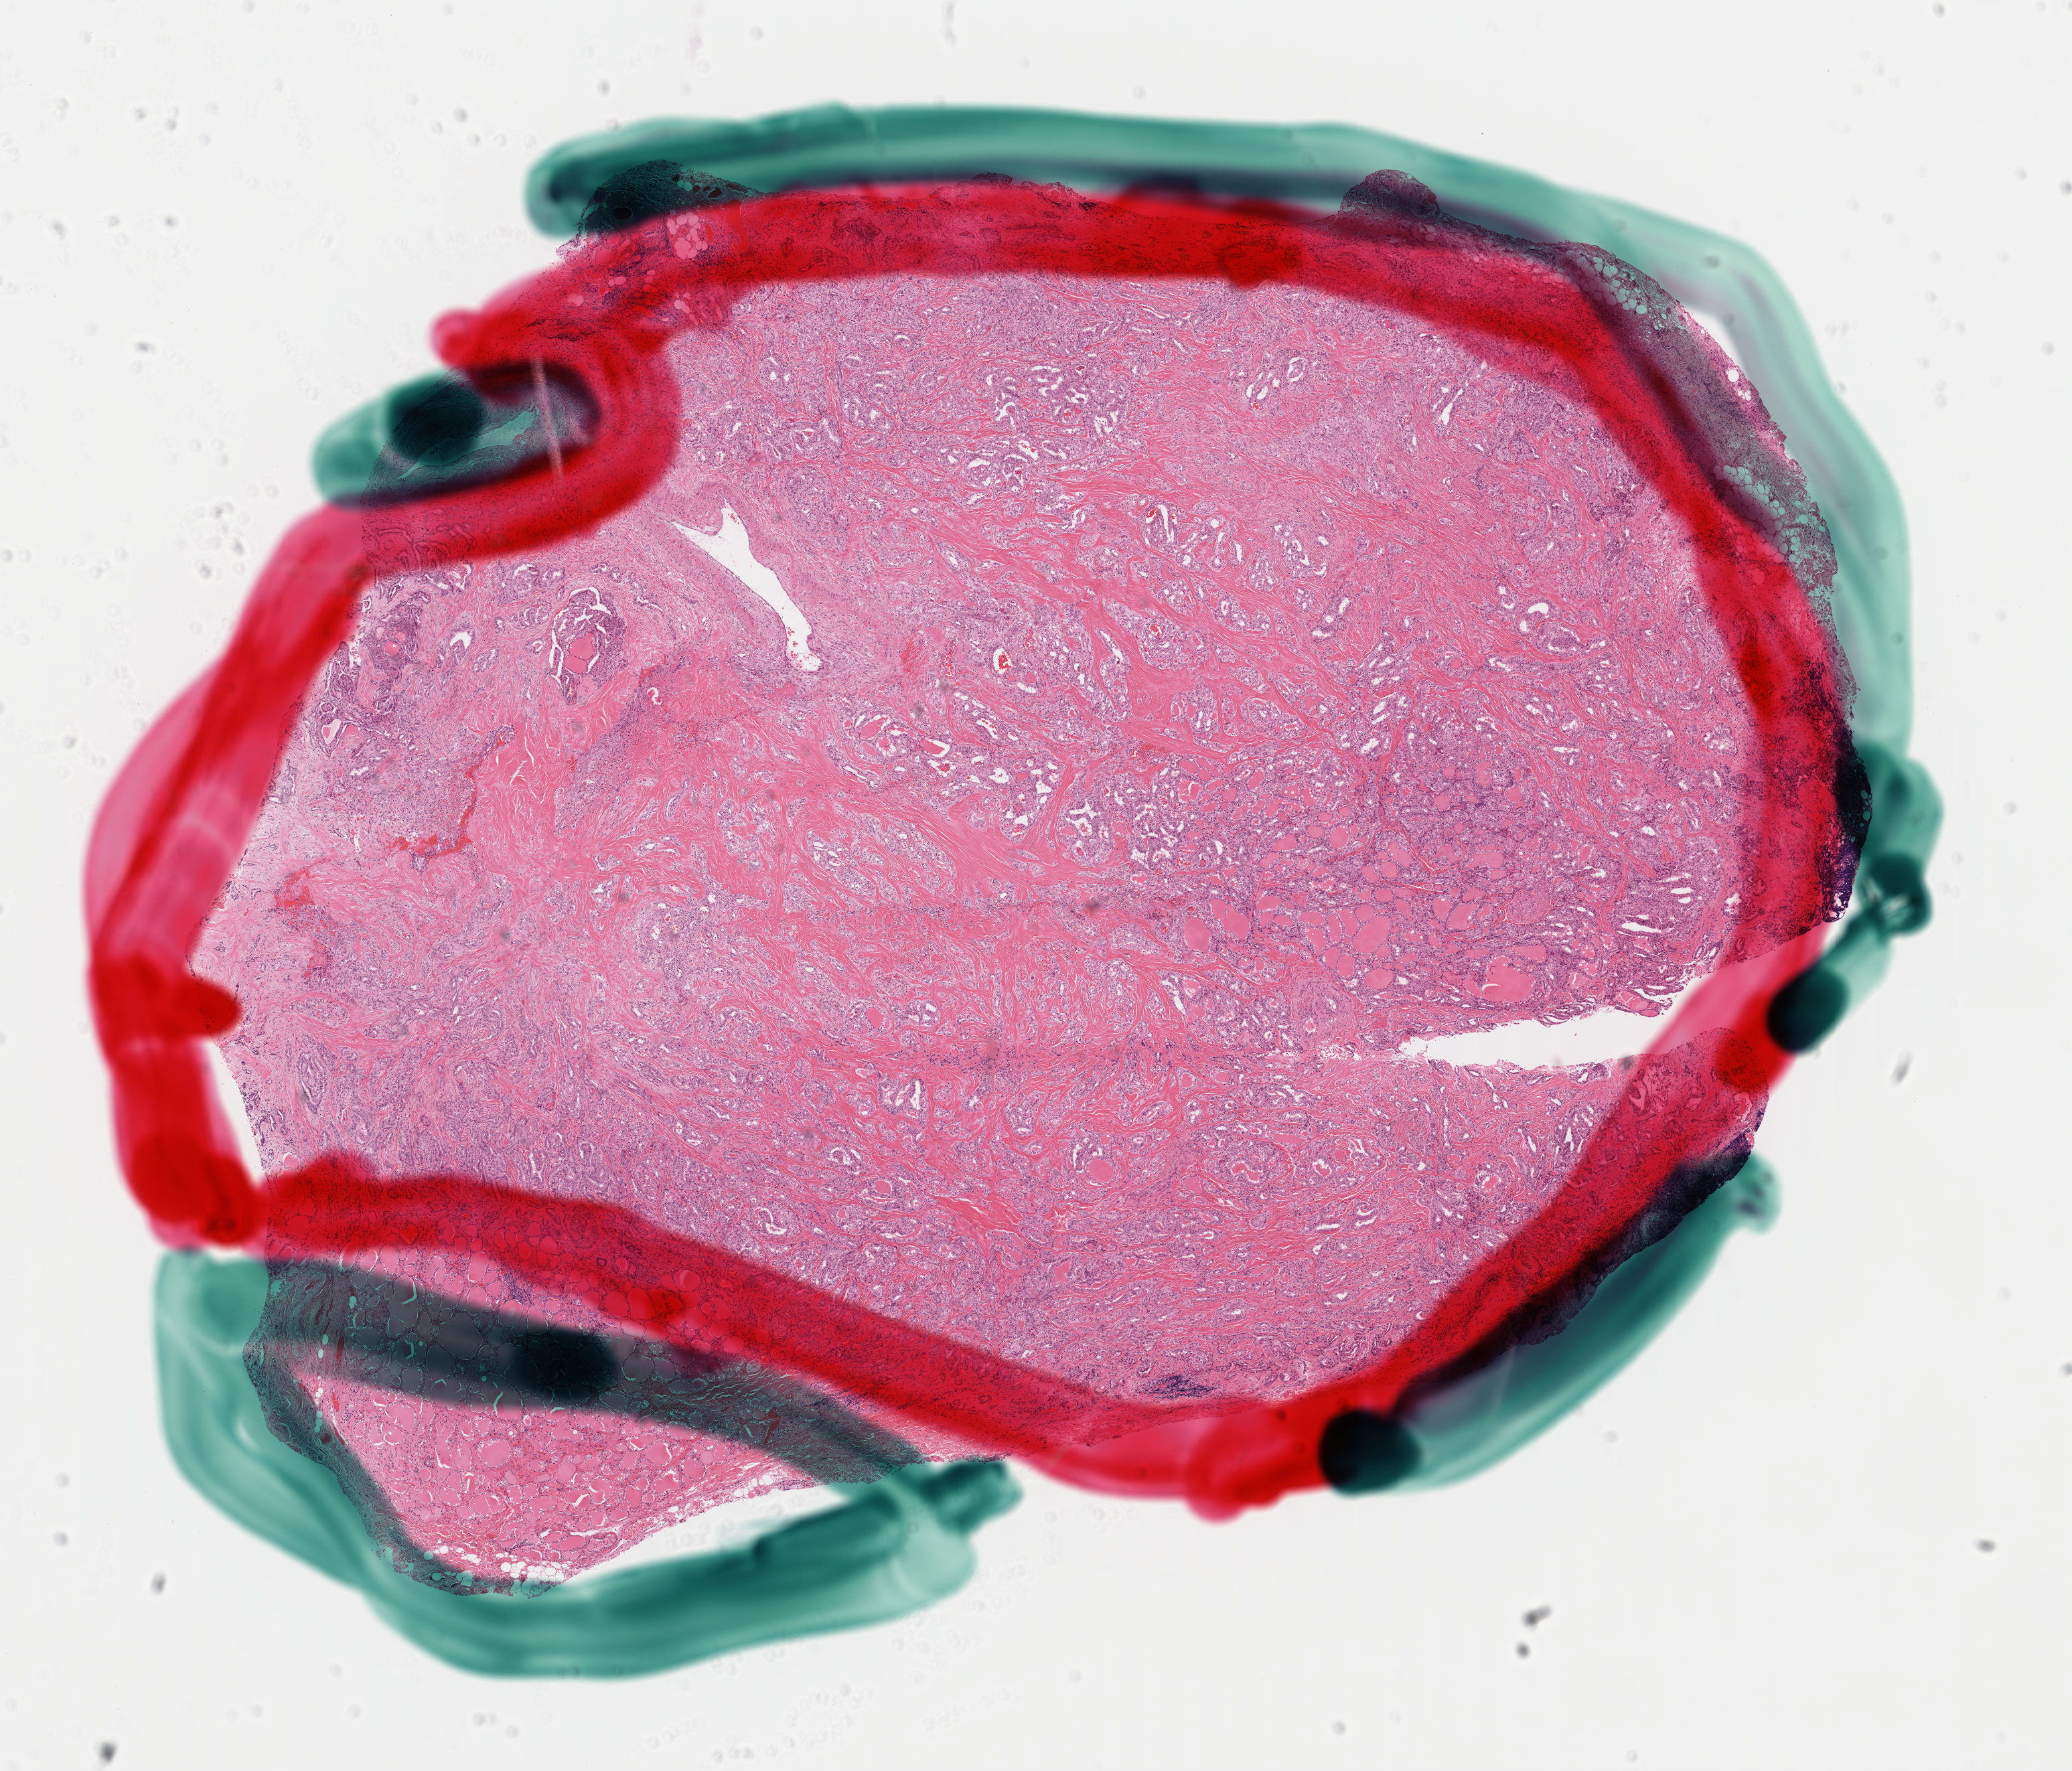
Digitized Hematoxylin and eosin (H&E) stained tissue section (whole slide) — a low-resolution overview of the entire scanned area, about 12.2 x 10.4 mm (from a 40x scan), formalin-fixed paraffin-embedded (FFPE) diagnostic section, sample: primary tumour, thyroid. Female patient; age at initial diagnosis 57 years.
- histologic diagnosis: Papillary adenocarcinoma, NOS (thyroid gland)
- AJCC pathologic stage: IVA (7th edition)